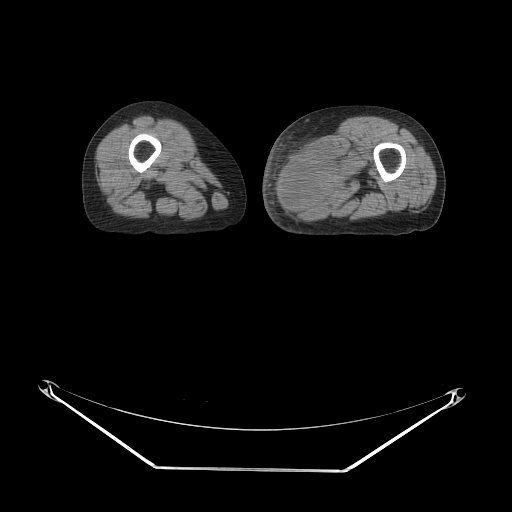
CT of an extremity soft-tissue mass (from a PET/CT study), one axial slice. Position 21 of 91 along the scan axis. Soft-tissue window (W 400 / L 40 HU). 512 × 512 image matrix. Female patient. From the clinical record (not read from this slice): histological type: pleomorphic leiomyosarcoma; grade: high; site of the primary tumour: left thigh.
Annotated regions visible in this slice (expert contour drawn on MRI and transferred to this co-registered scan by the dataset authors):
- gross tumour volume including surrounding oedema: bounding box <281,132,364,211> (left, top, right, bottom; pixels)
- gross tumour volume (mass): <281,151,350,211>